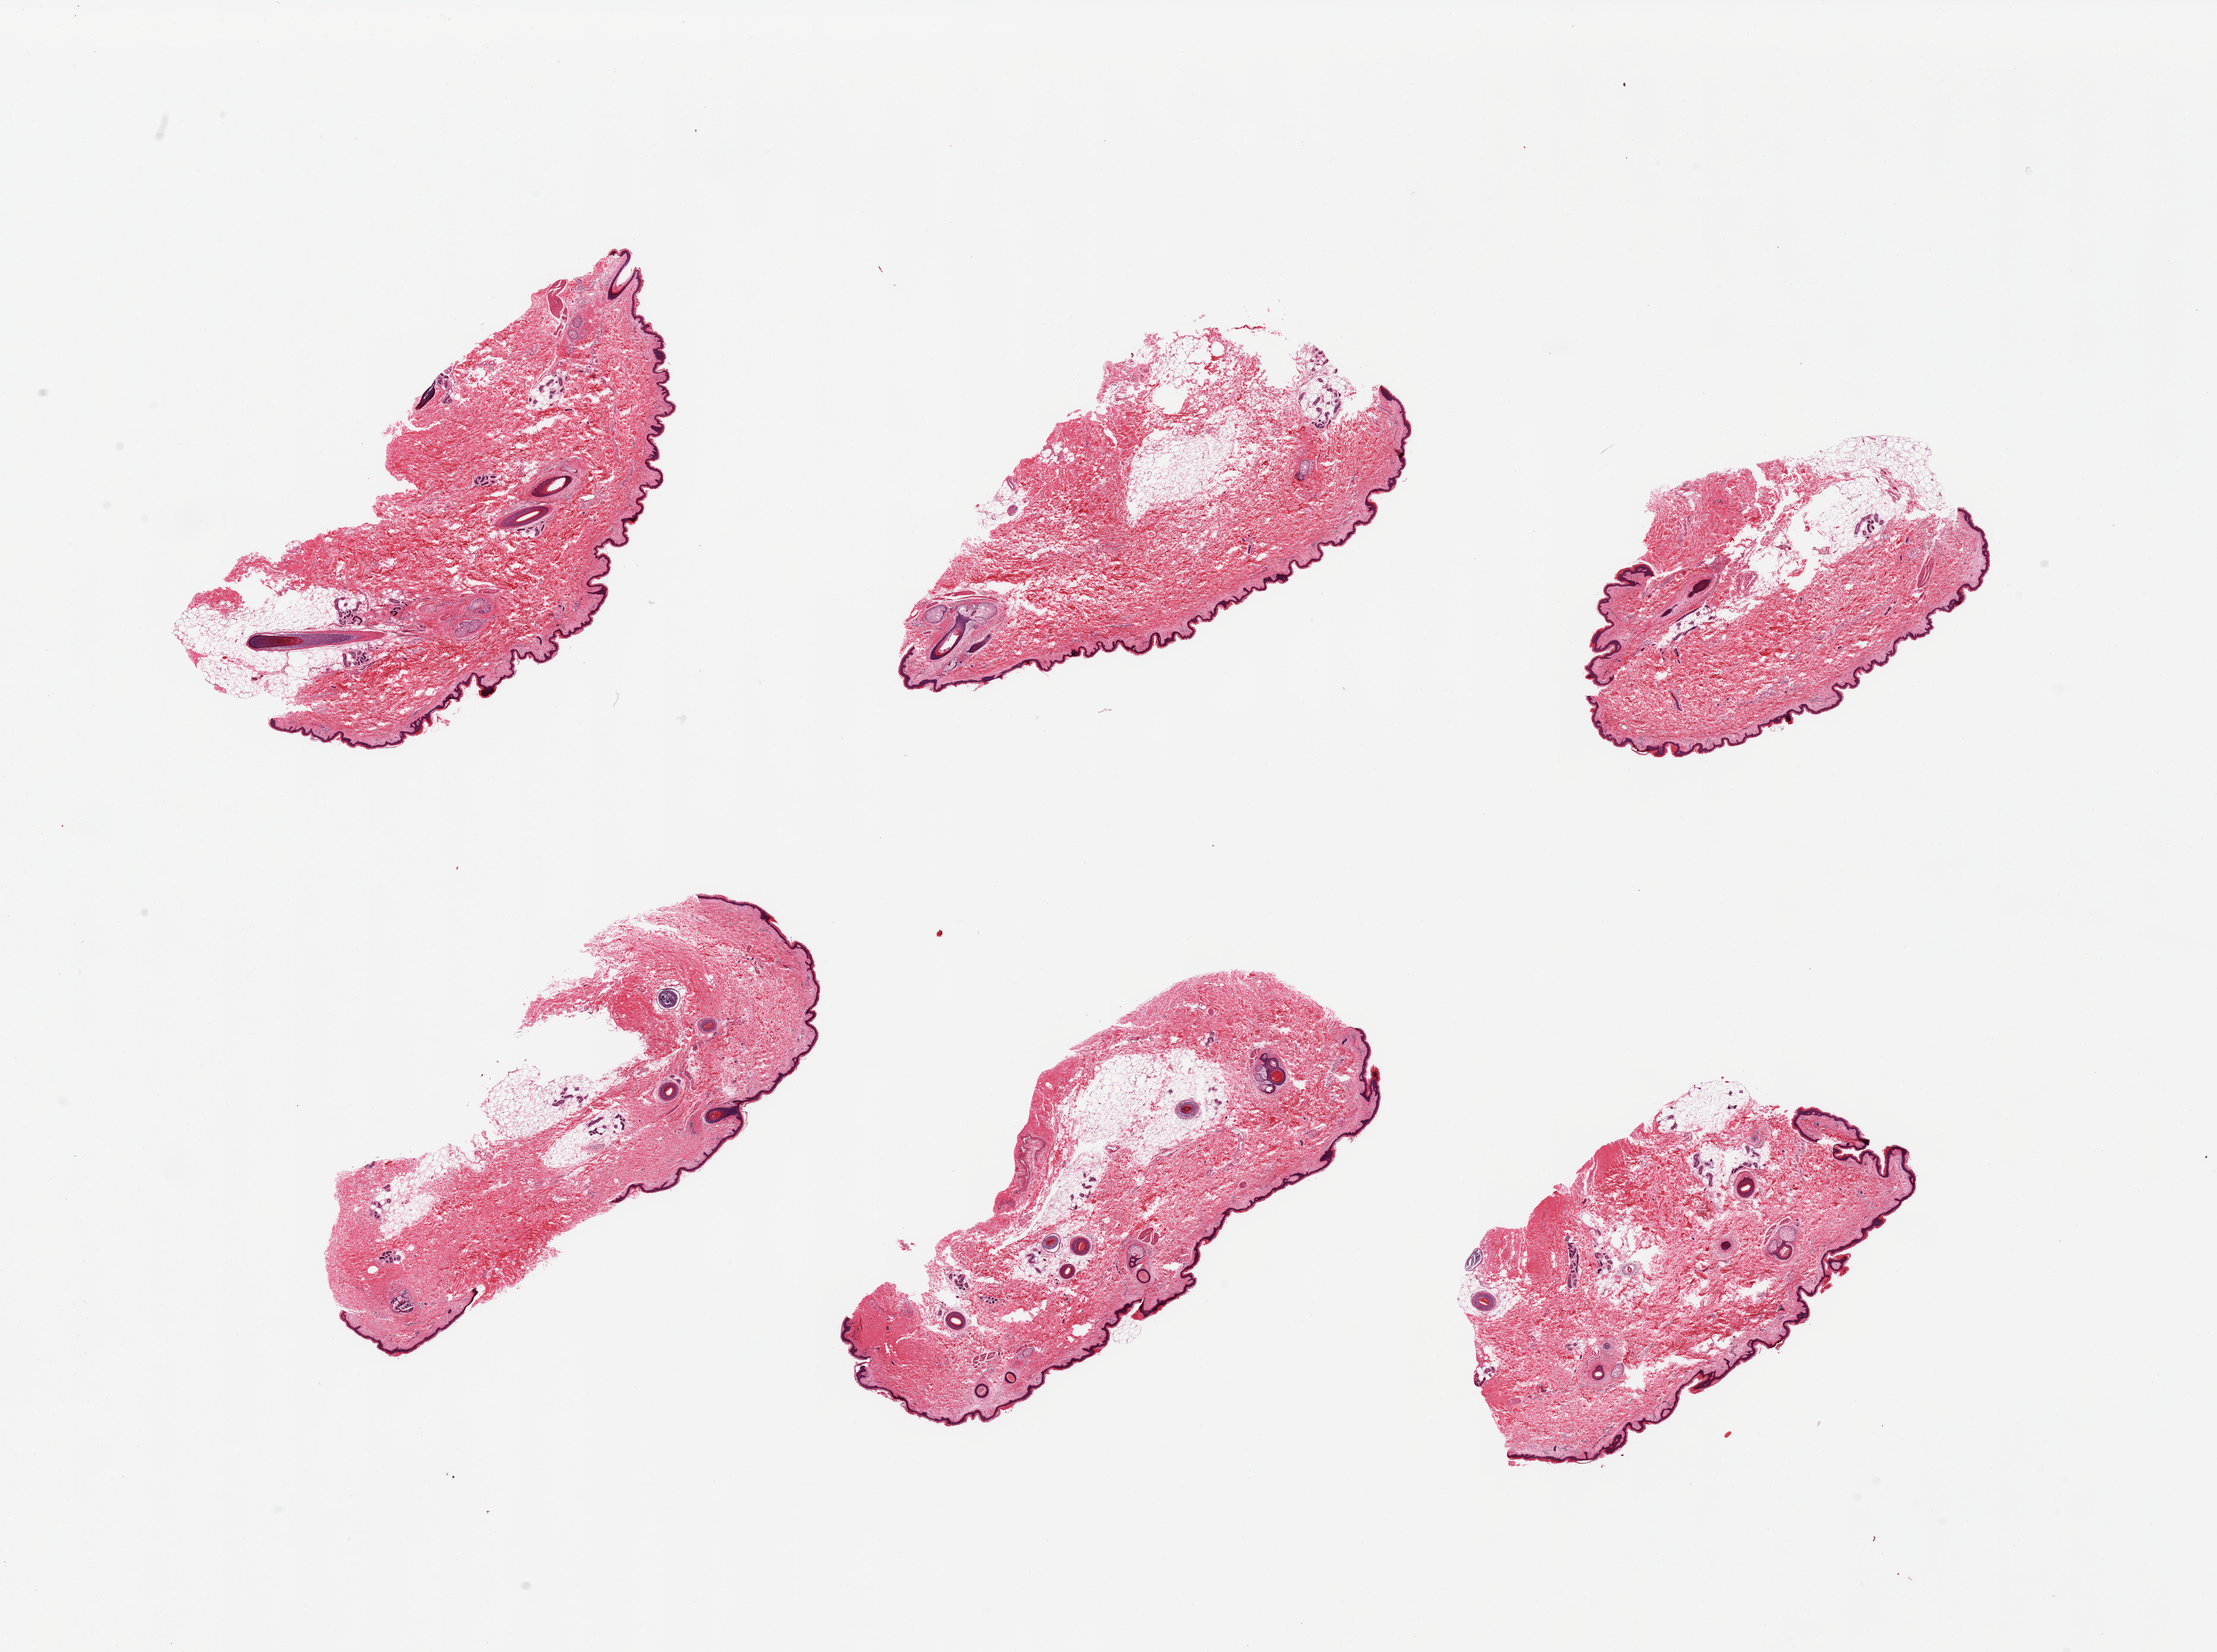
Digitized haematoxylin and eosin-stained section — shown as a low-resolution overview of the whole scanned area (about 29.5 x 22.0 mm), PAXgene-fixed paraffin-embedded (PFPE) section, target tissue: skin of suprapubic region, tissue donor sample.
Review note (as recorded): 6 pieces, minimal fat, squamous epitheliums is ~50 microns.